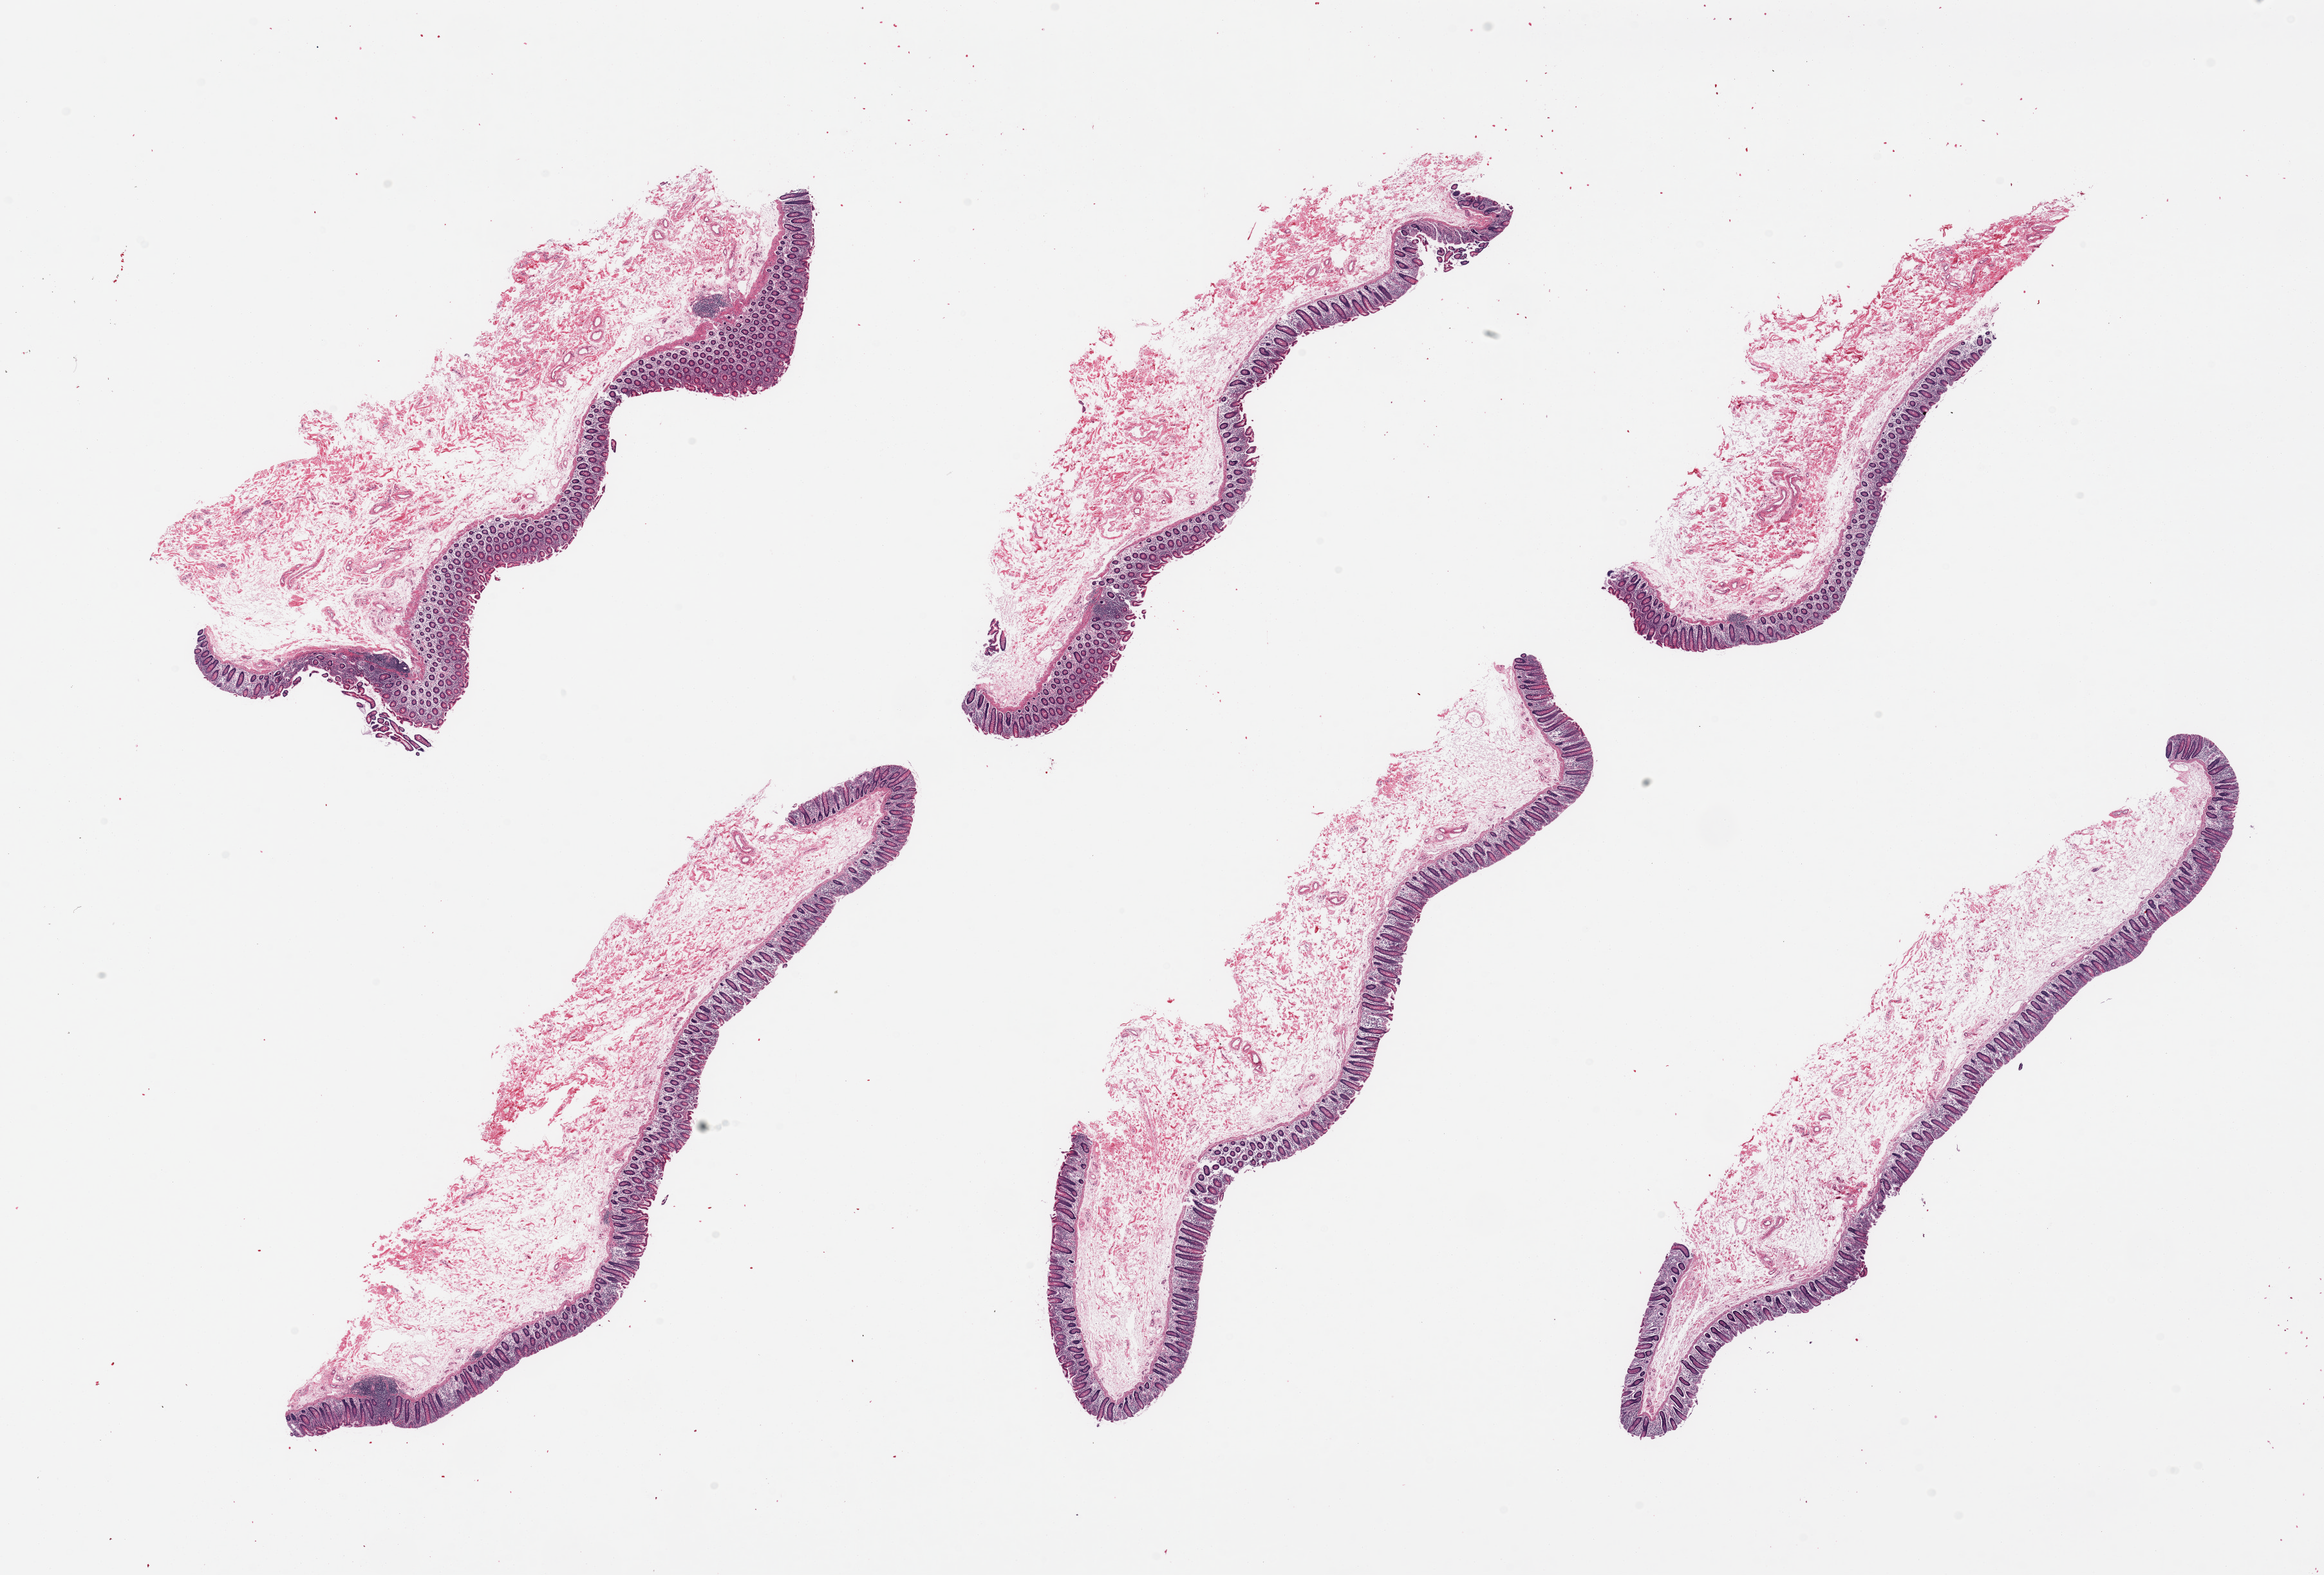
Hematoxylin and eosin (H&E) whole-slide image, brightfield — low-resolution overview of the scanned area, about 28.5 x 19.4 mm (slide scanned at 20x). Female donor.
Specimen: PAXgene-fixed, paraffin-embedded tissue; target tissue: ileum; tissue donor sample.